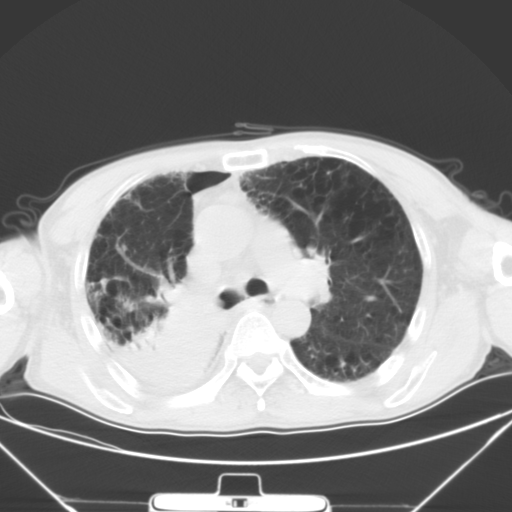
Chest CT, one axial slice. Position 30 of 50 along the scan axis. Lung window (W 1500 / L -600 HU). 5 mm slice thickness. 512 × 512 image matrix, field of view 373 × 373 mm. Male patient, age 65 years. Case-level facts recorded for this patient, not image findings: clinical TNM (as recorded): T3 N1 M1a.
Annotated regions visible in this slice (rectangle marked by the reading radiologist):
- lung tumour (recorded histology: squamous cell carcinoma): box from (x=118, y=280) to (x=225, y=392) px